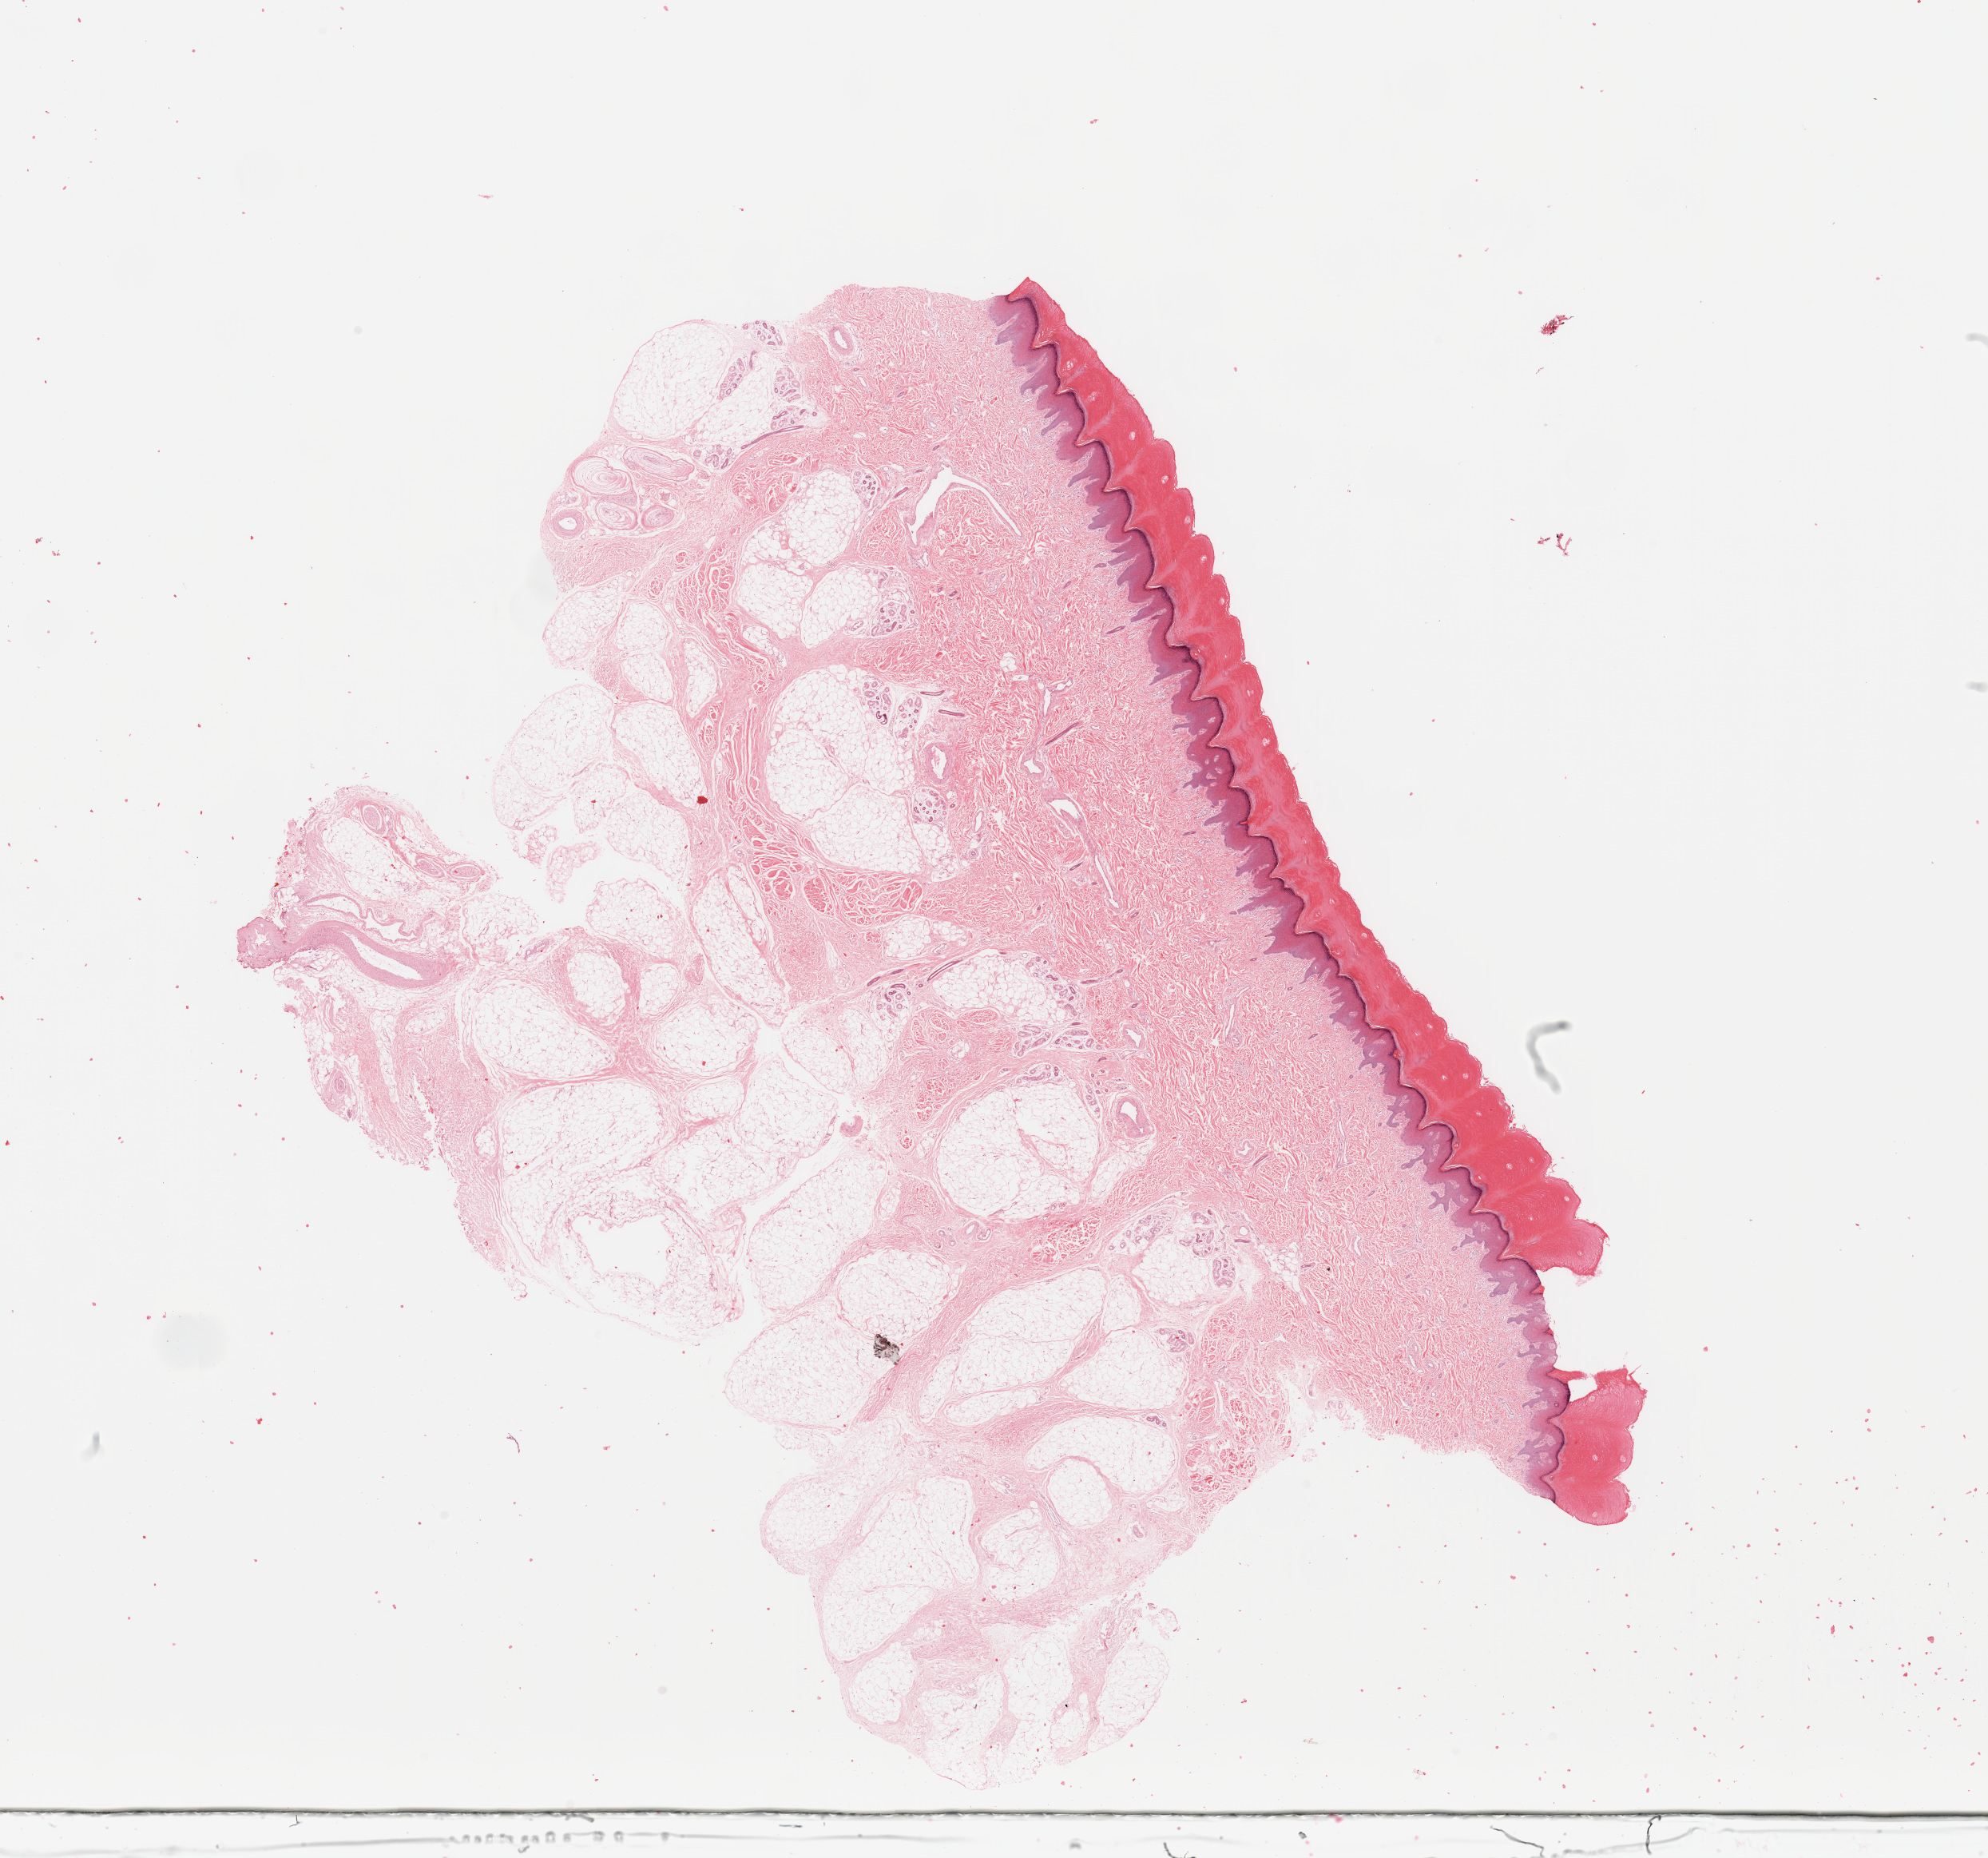
Digitized H&E-stained tissue section (whole slide) — whole scanned area (about 19.7 x 18.4 mm) shown as a low-resolution overview. Normal (non-tumour) tissue (melanoma cohort); sampled site not recorded. 69-year-old male patient.
This section: normal (non-tumour) tissue from the same patient. Patient diagnosis: Malignant melanoma, NOS.